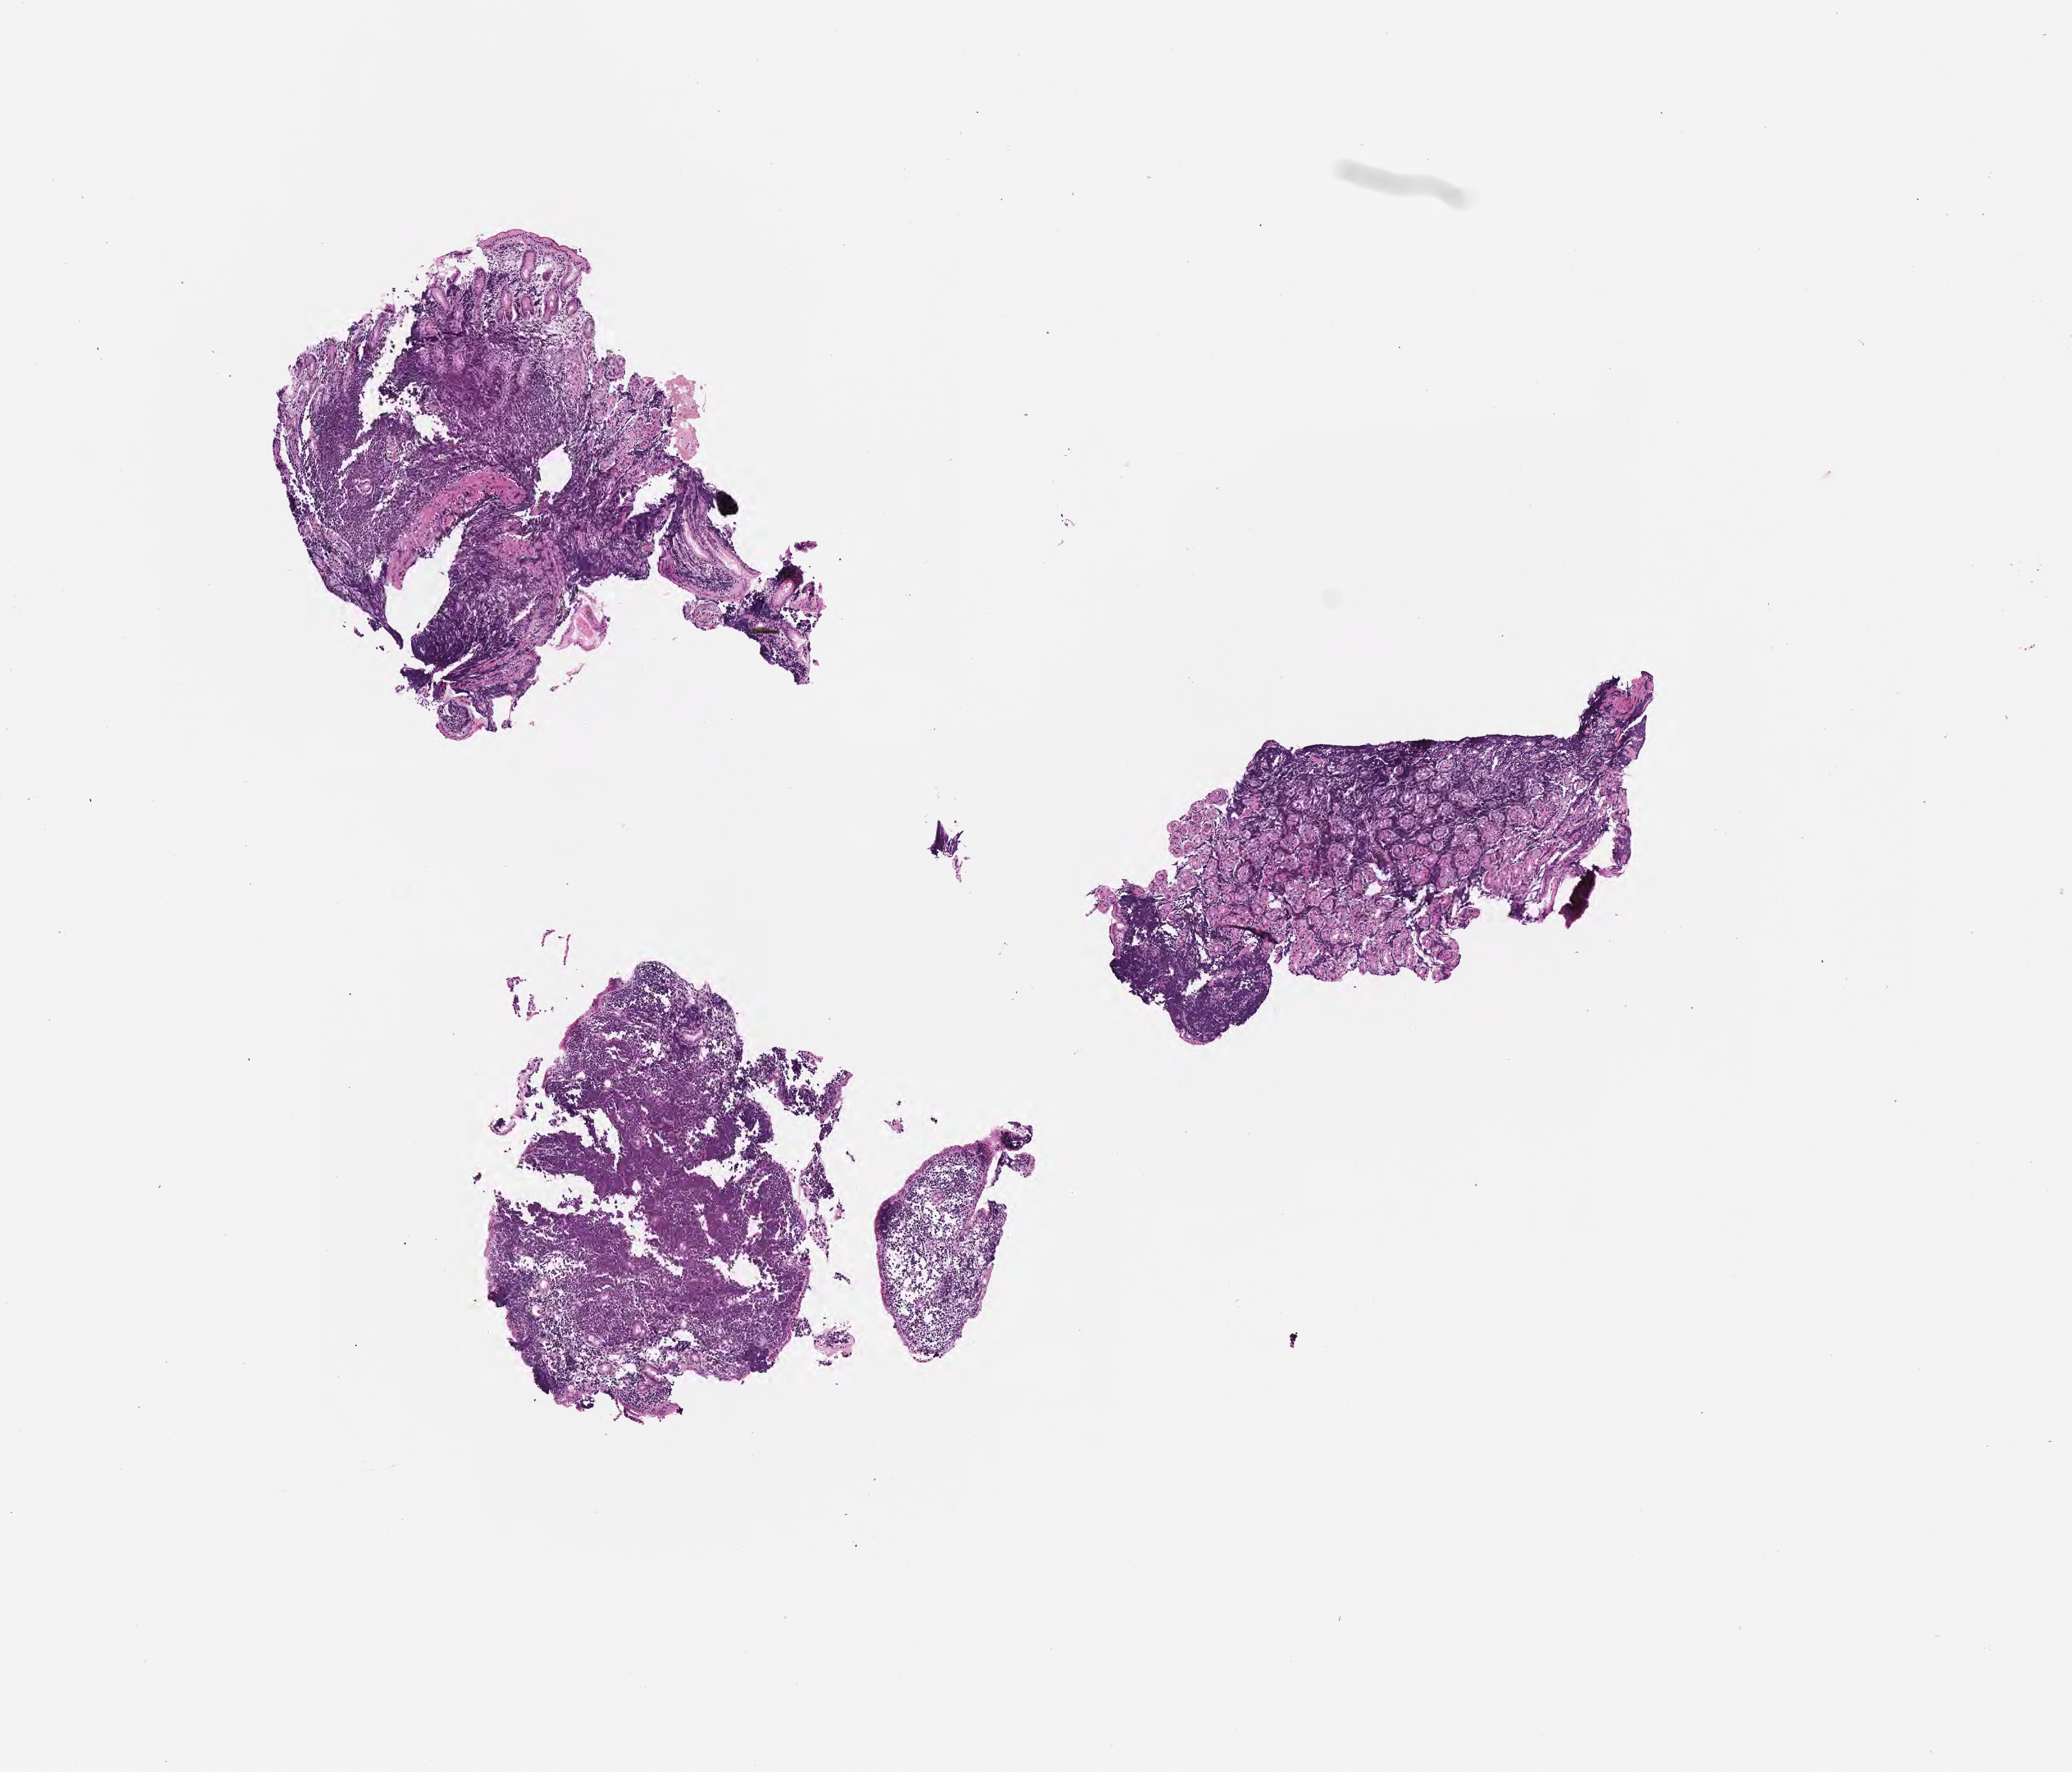
Digitized haematoxylin and eosin-stained section, low-resolution overview of the scanned area, about 6.5 x 5.6 mm. Formalin-fixed paraffin-embedded section. Primary tumor. Female patient, age 45 years. Composition of this section per pathologist review: tumor cells 85%, tumor nuclei 95%, stromal cells 10%, necrosis 5%, normal cells 0%. Infiltration values recorded for this section: lymphocyte infiltration 50%, monocyte infiltration 30%, neutrophil infiltration 5%.
Diagnosis: Burkitt lymphoma, NOS. Section: top of the tissue portion. Ann Arbor stage (patient): Stage IV.